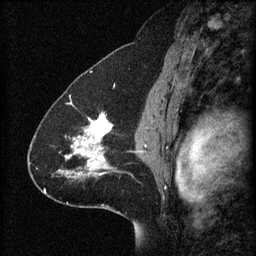
Breast MRI (dynamic contrast-enhanced), one sagittal slice; slice 41 of 60 in the series (ordered by position); 3 images stored at this slice position (order not interpretable as contrast timing); 1.5 T; TE 4.2 ms, TR 8.2 ms; 256 × 256 image matrix, field of view 200 × 200 mm. Female patient, age 41 years.
Structures marked on this image (semi-automatically segmented with operator editing):
- analysis volume of interest (the breast-tissue region the enhancement analysis was run in; not a lesion): box from (x=58, y=114) to (x=122, y=179) px
- tumour enhancement mask (voxels above the 70 % enhancement threshold inside the analysis volume of interest): (x=60, y=114)–(x=114, y=177)